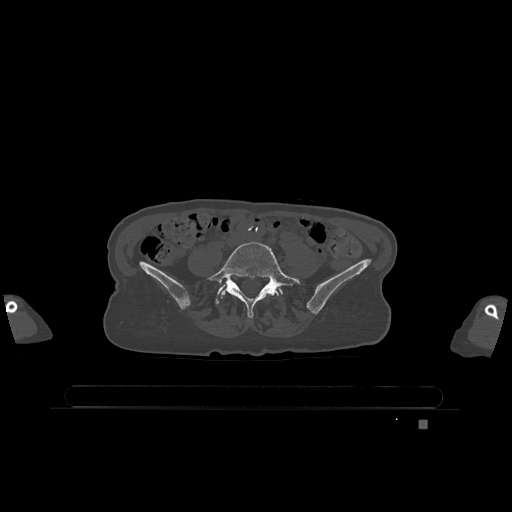
CT including the spine, one axial slice; slice 243 of 1317 in the series (ordered by position); bone window (W 1800 / L 400 HU); 512 × 512 image matrix, field of view 500 × 500 mm. Patient: female, 74 years. From the clinical record (not read from this slice): primary cancer: lung.
Annotated regions visible in this slice (semi-automatically segmented with operator editing):
- L5 vertebra: bounding box (x1, y1, x2, y2) in pixels: (207, 242, 301, 318)